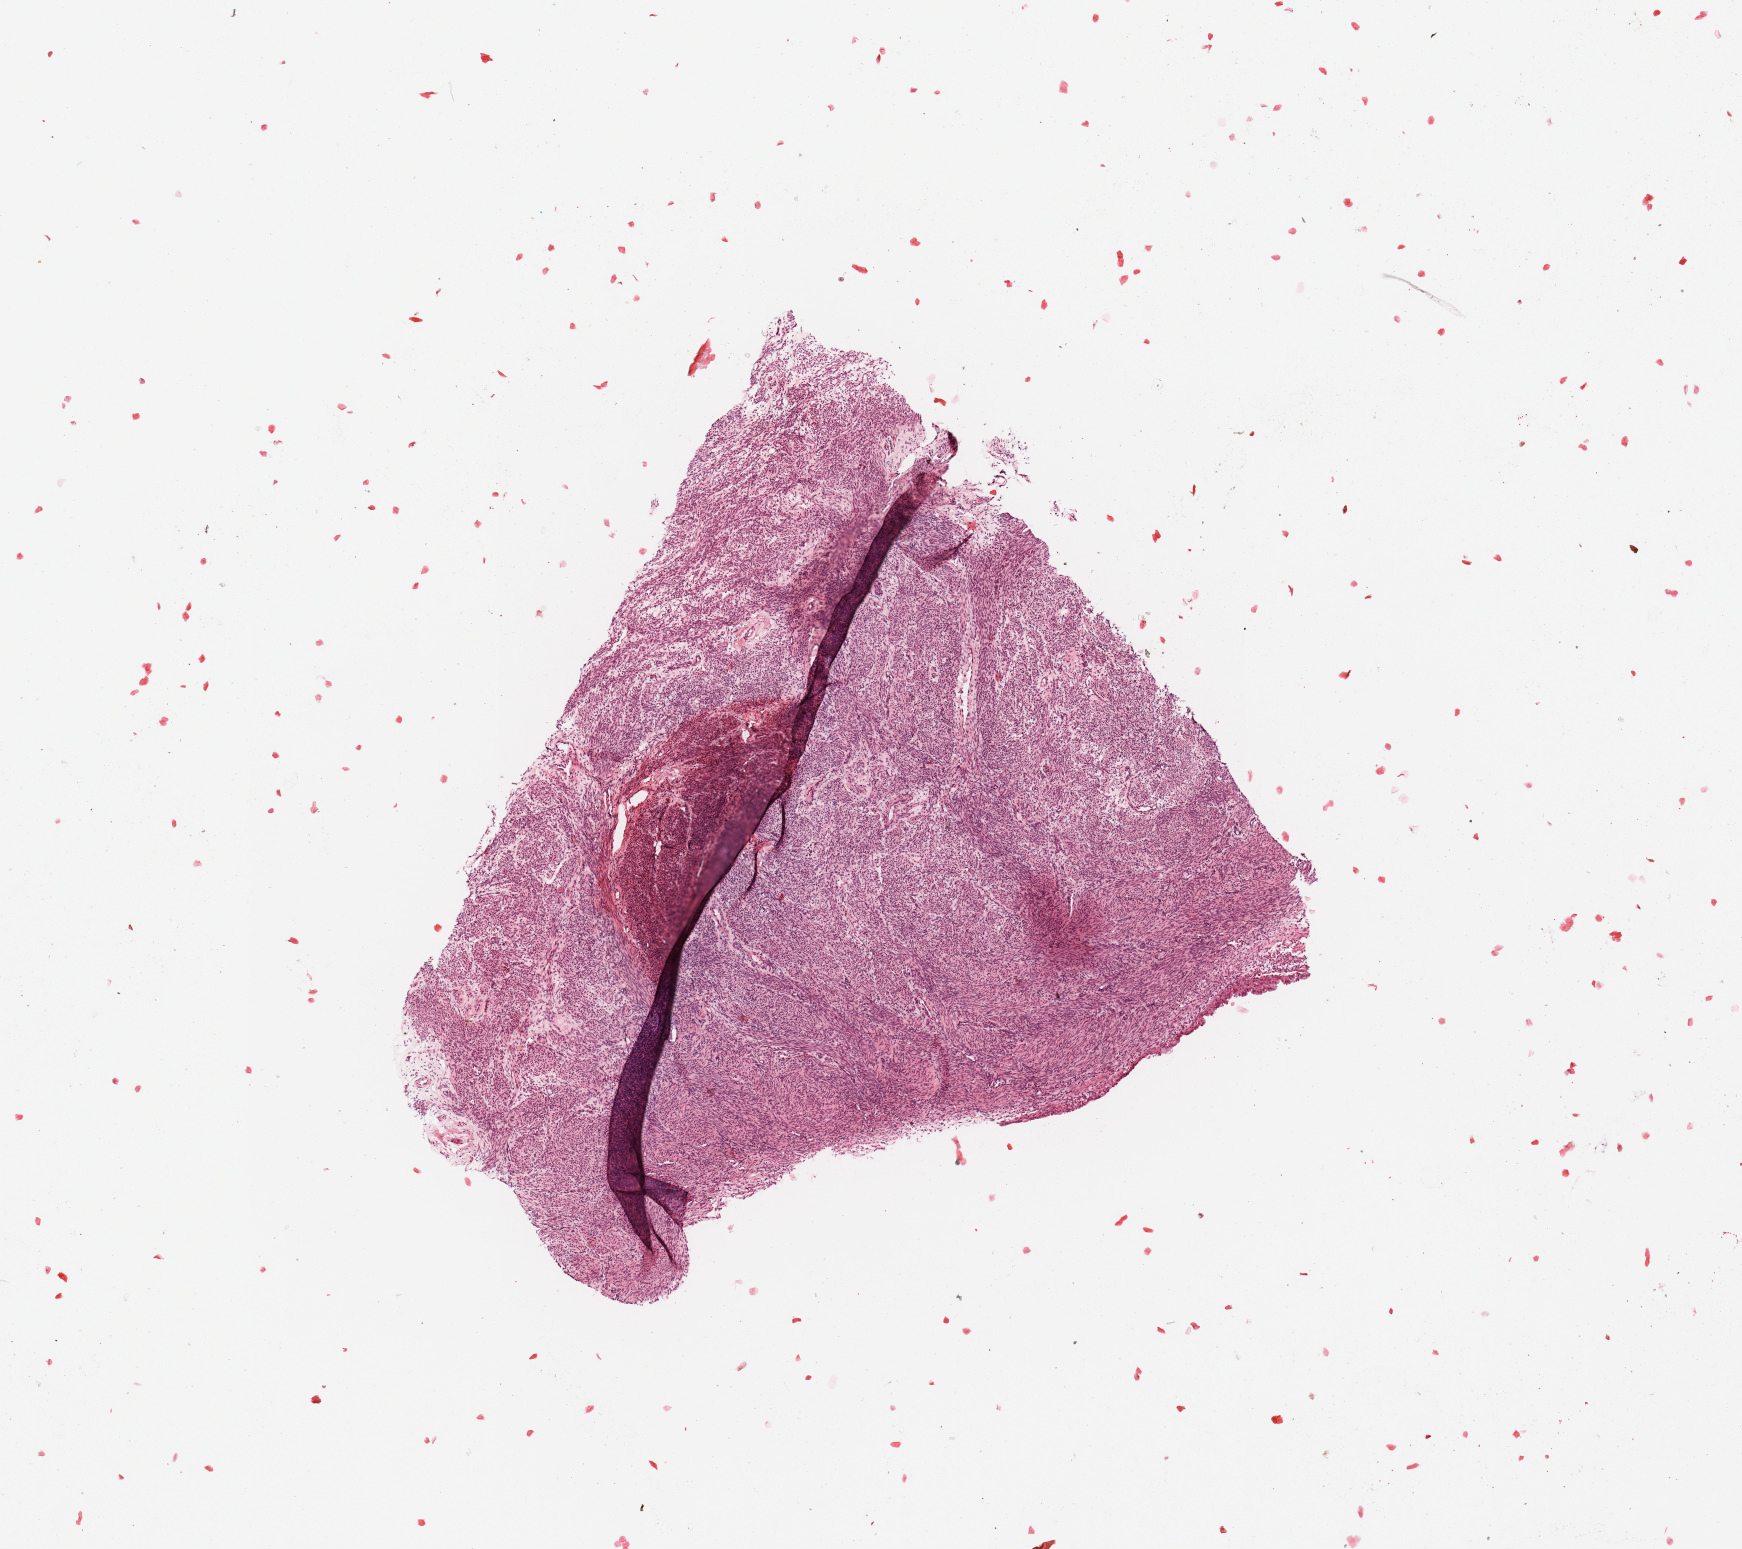
Digitized H&E-stained tissue section (whole slide), a low-resolution overview of the entire scanned area, about 6.9 x 6.1 mm (acquisition: 20x scan), uterus, normal (non-tumour) tissue. Patient: female, age 83 years.
- this section: normal (non-tumour) tissue from the same patient
- patient diagnosis: Endometrioid adenocarcinoma, NOS